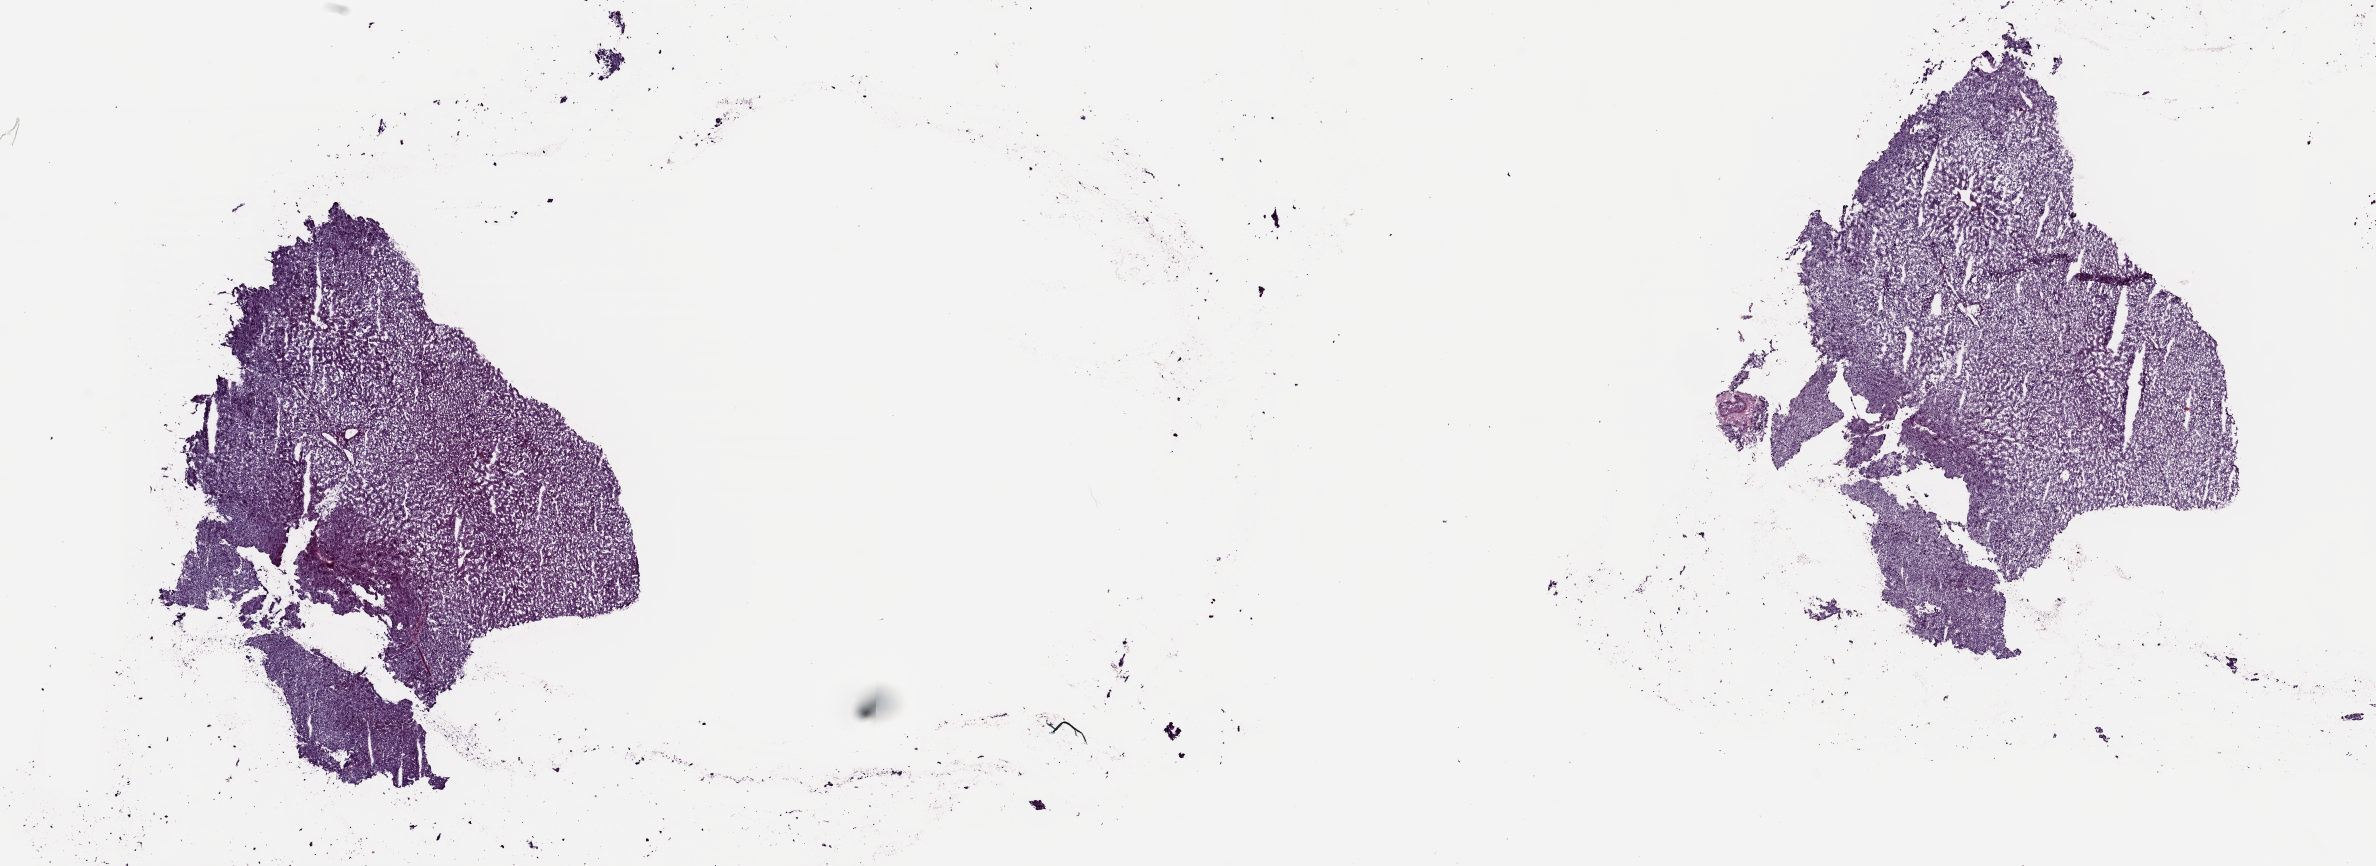
H&E whole-slide image — whole scanned area (about 18.8 x 6.9 mm, acquisition: 20x scan) shown as a low-resolution overview. Frozen section. Sample: solid tissue normal (non-tumour tissue), liver. Male patient; age at initial diagnosis 80 years. Slide review estimates, as recorded: tumour cells 0%, tumour nuclei 0%, normal cells 85%, stromal cells 15%, necrosis 0%. Inflammatory infiltration, as recorded: lymphocyte infiltration 3%, monocyte infiltration 0%, neutrophil infiltration 0%.
This section: solid tissue normal (non-tumour) sample from the same patient. Patient diagnosis: Hepatocellular carcinoma, NOS.